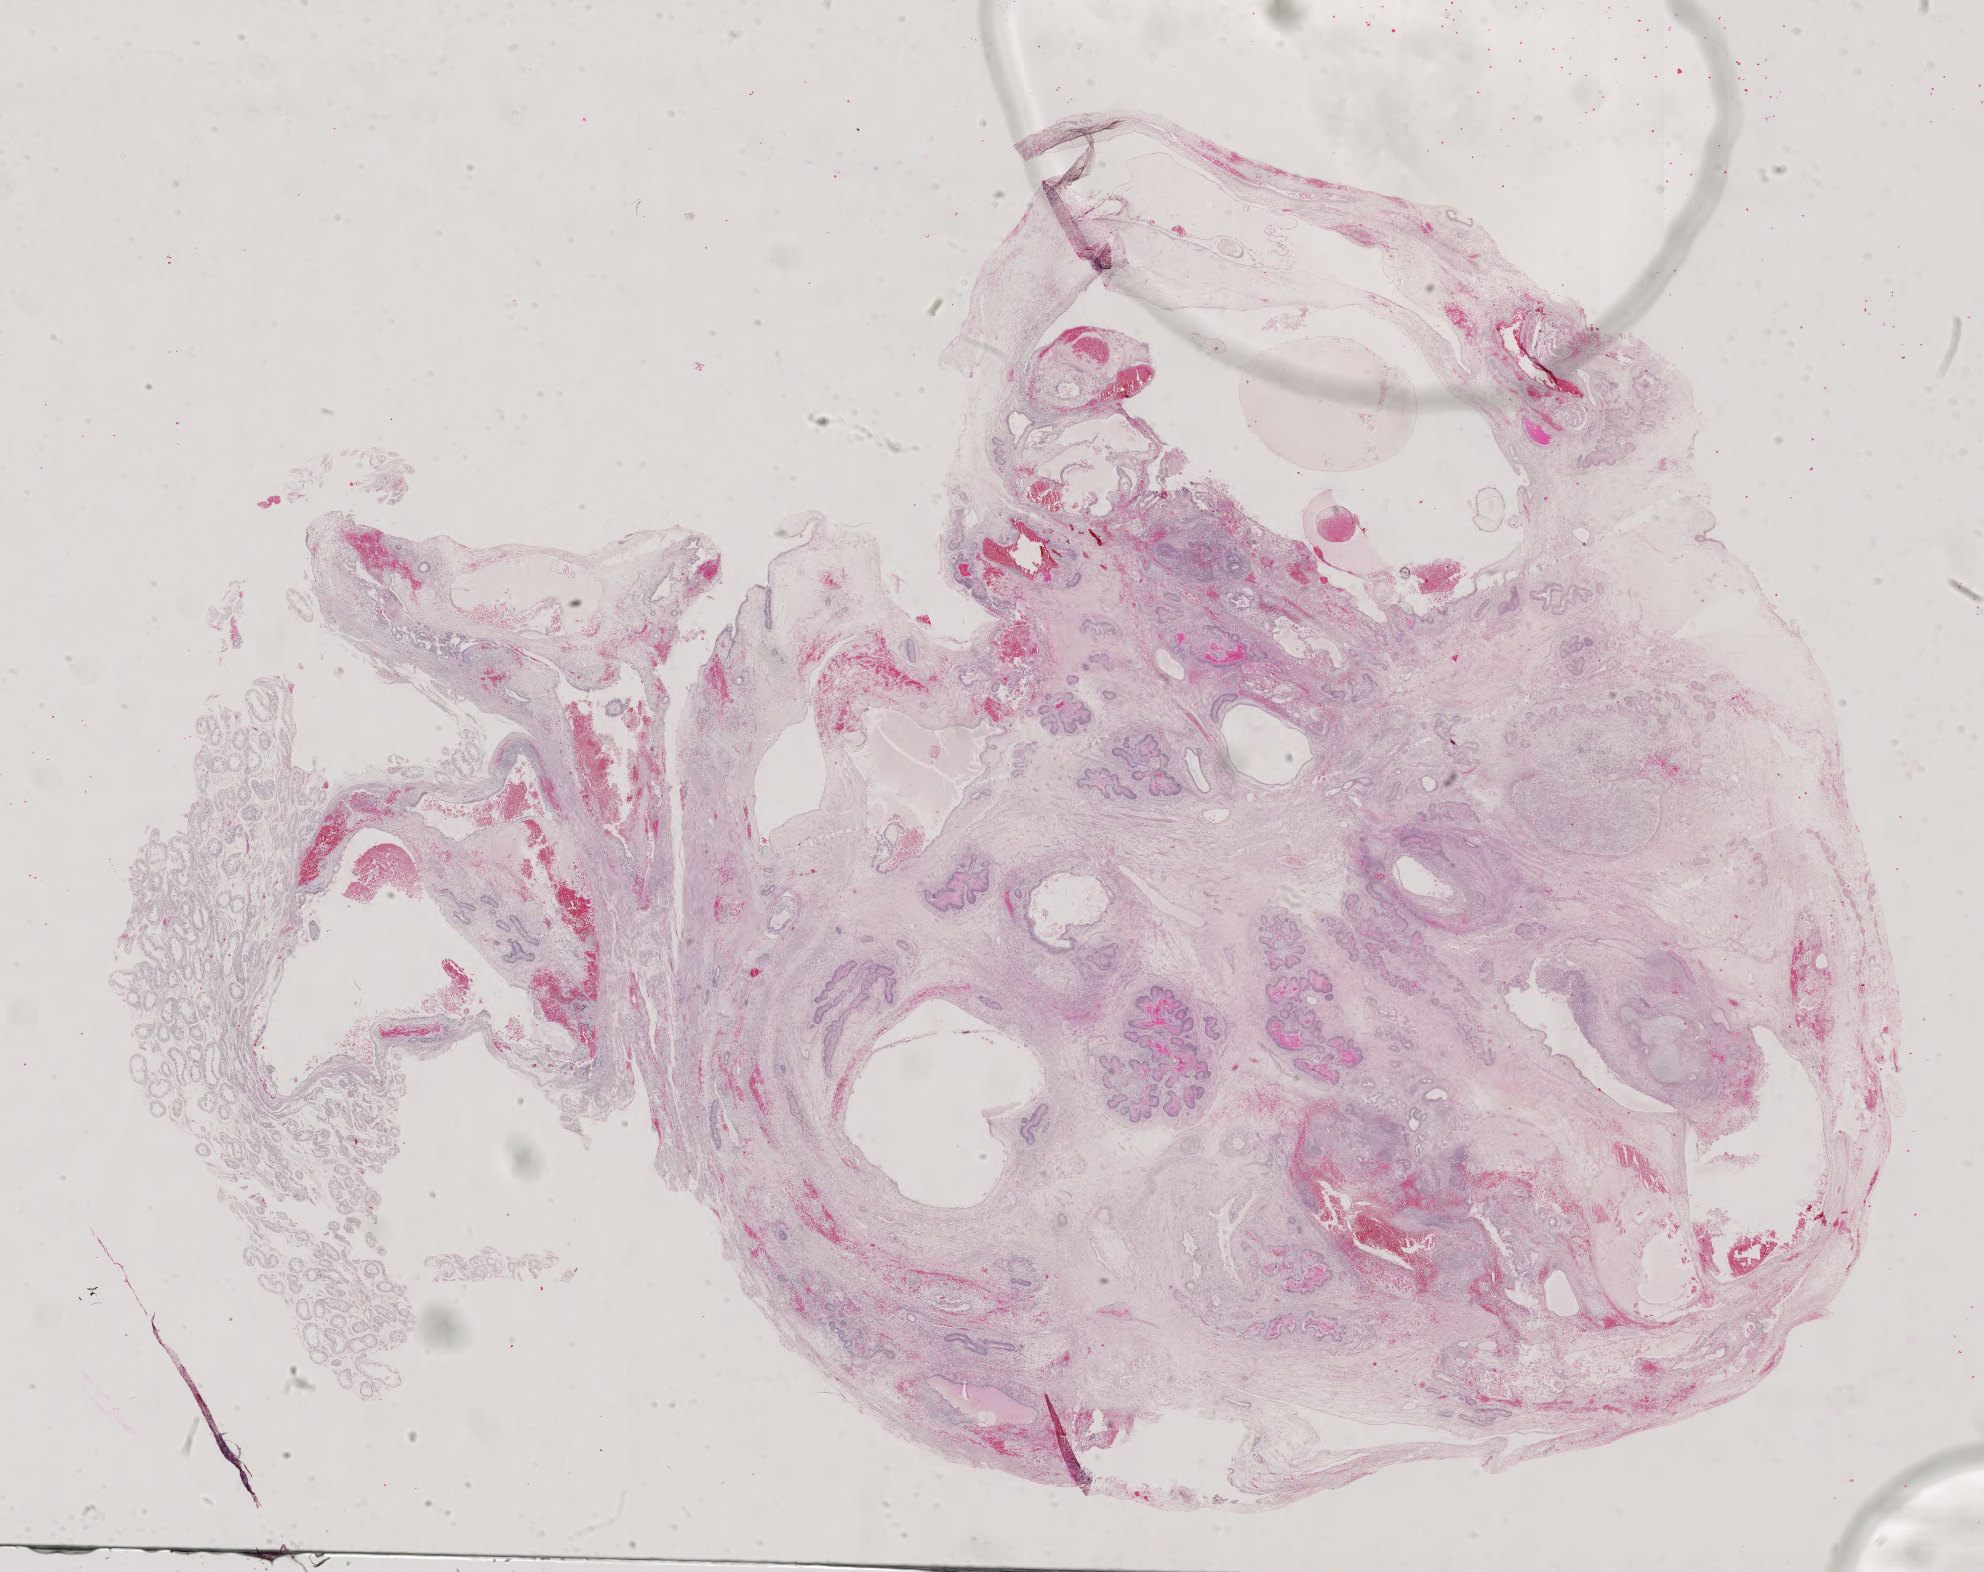
Digitized Hematoxylin and eosin (H&E) stained tissue section (whole slide), low-resolution overview of the scanned area, about 28.9 x 22.9 mm (slide scanned at 40x). Formalin-fixed paraffin-embedded (FFPE) diagnostic section. Testis, primary tumour sample. Male patient; age at initial diagnosis 20 years.
AJCC pathologic stage: IIIC (6th edition). Laterality: left. Histologic diagnosis: Mixed germ cell tumor.